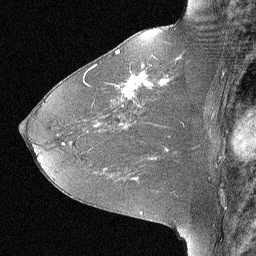
Breast MRI (dynamic contrast-enhanced), one sagittal slice; position 37 of 64 along the scan axis; dynamic contrast-enhanced study with each time point stored as its own series, time point 2 of 3 at this slice position (early post-contrast, ordered by acquisition time); 1.5 T; TE 4 ms, TR 30 ms; 2.25 mm slice thickness; 256 × 256 image matrix. Patient: female, 46 years. From the clinical record (not read from this slice): setting: breast cancer imaged before/during neoadjuvant chemotherapy; receptor status: HR-positive, HER2-negative.
Outlined on this slice (semi-automatic segmentation, software-assisted and operator-edited):
- analysis volume of interest (the breast-tissue region the enhancement analysis was run in; not a lesion): box from (x=106, y=43) to (x=184, y=119) px
- tumour enhancement mask (voxels above the 90 % enhancement threshold inside the analysis volume of interest): (x=117, y=51)–(x=166, y=99)